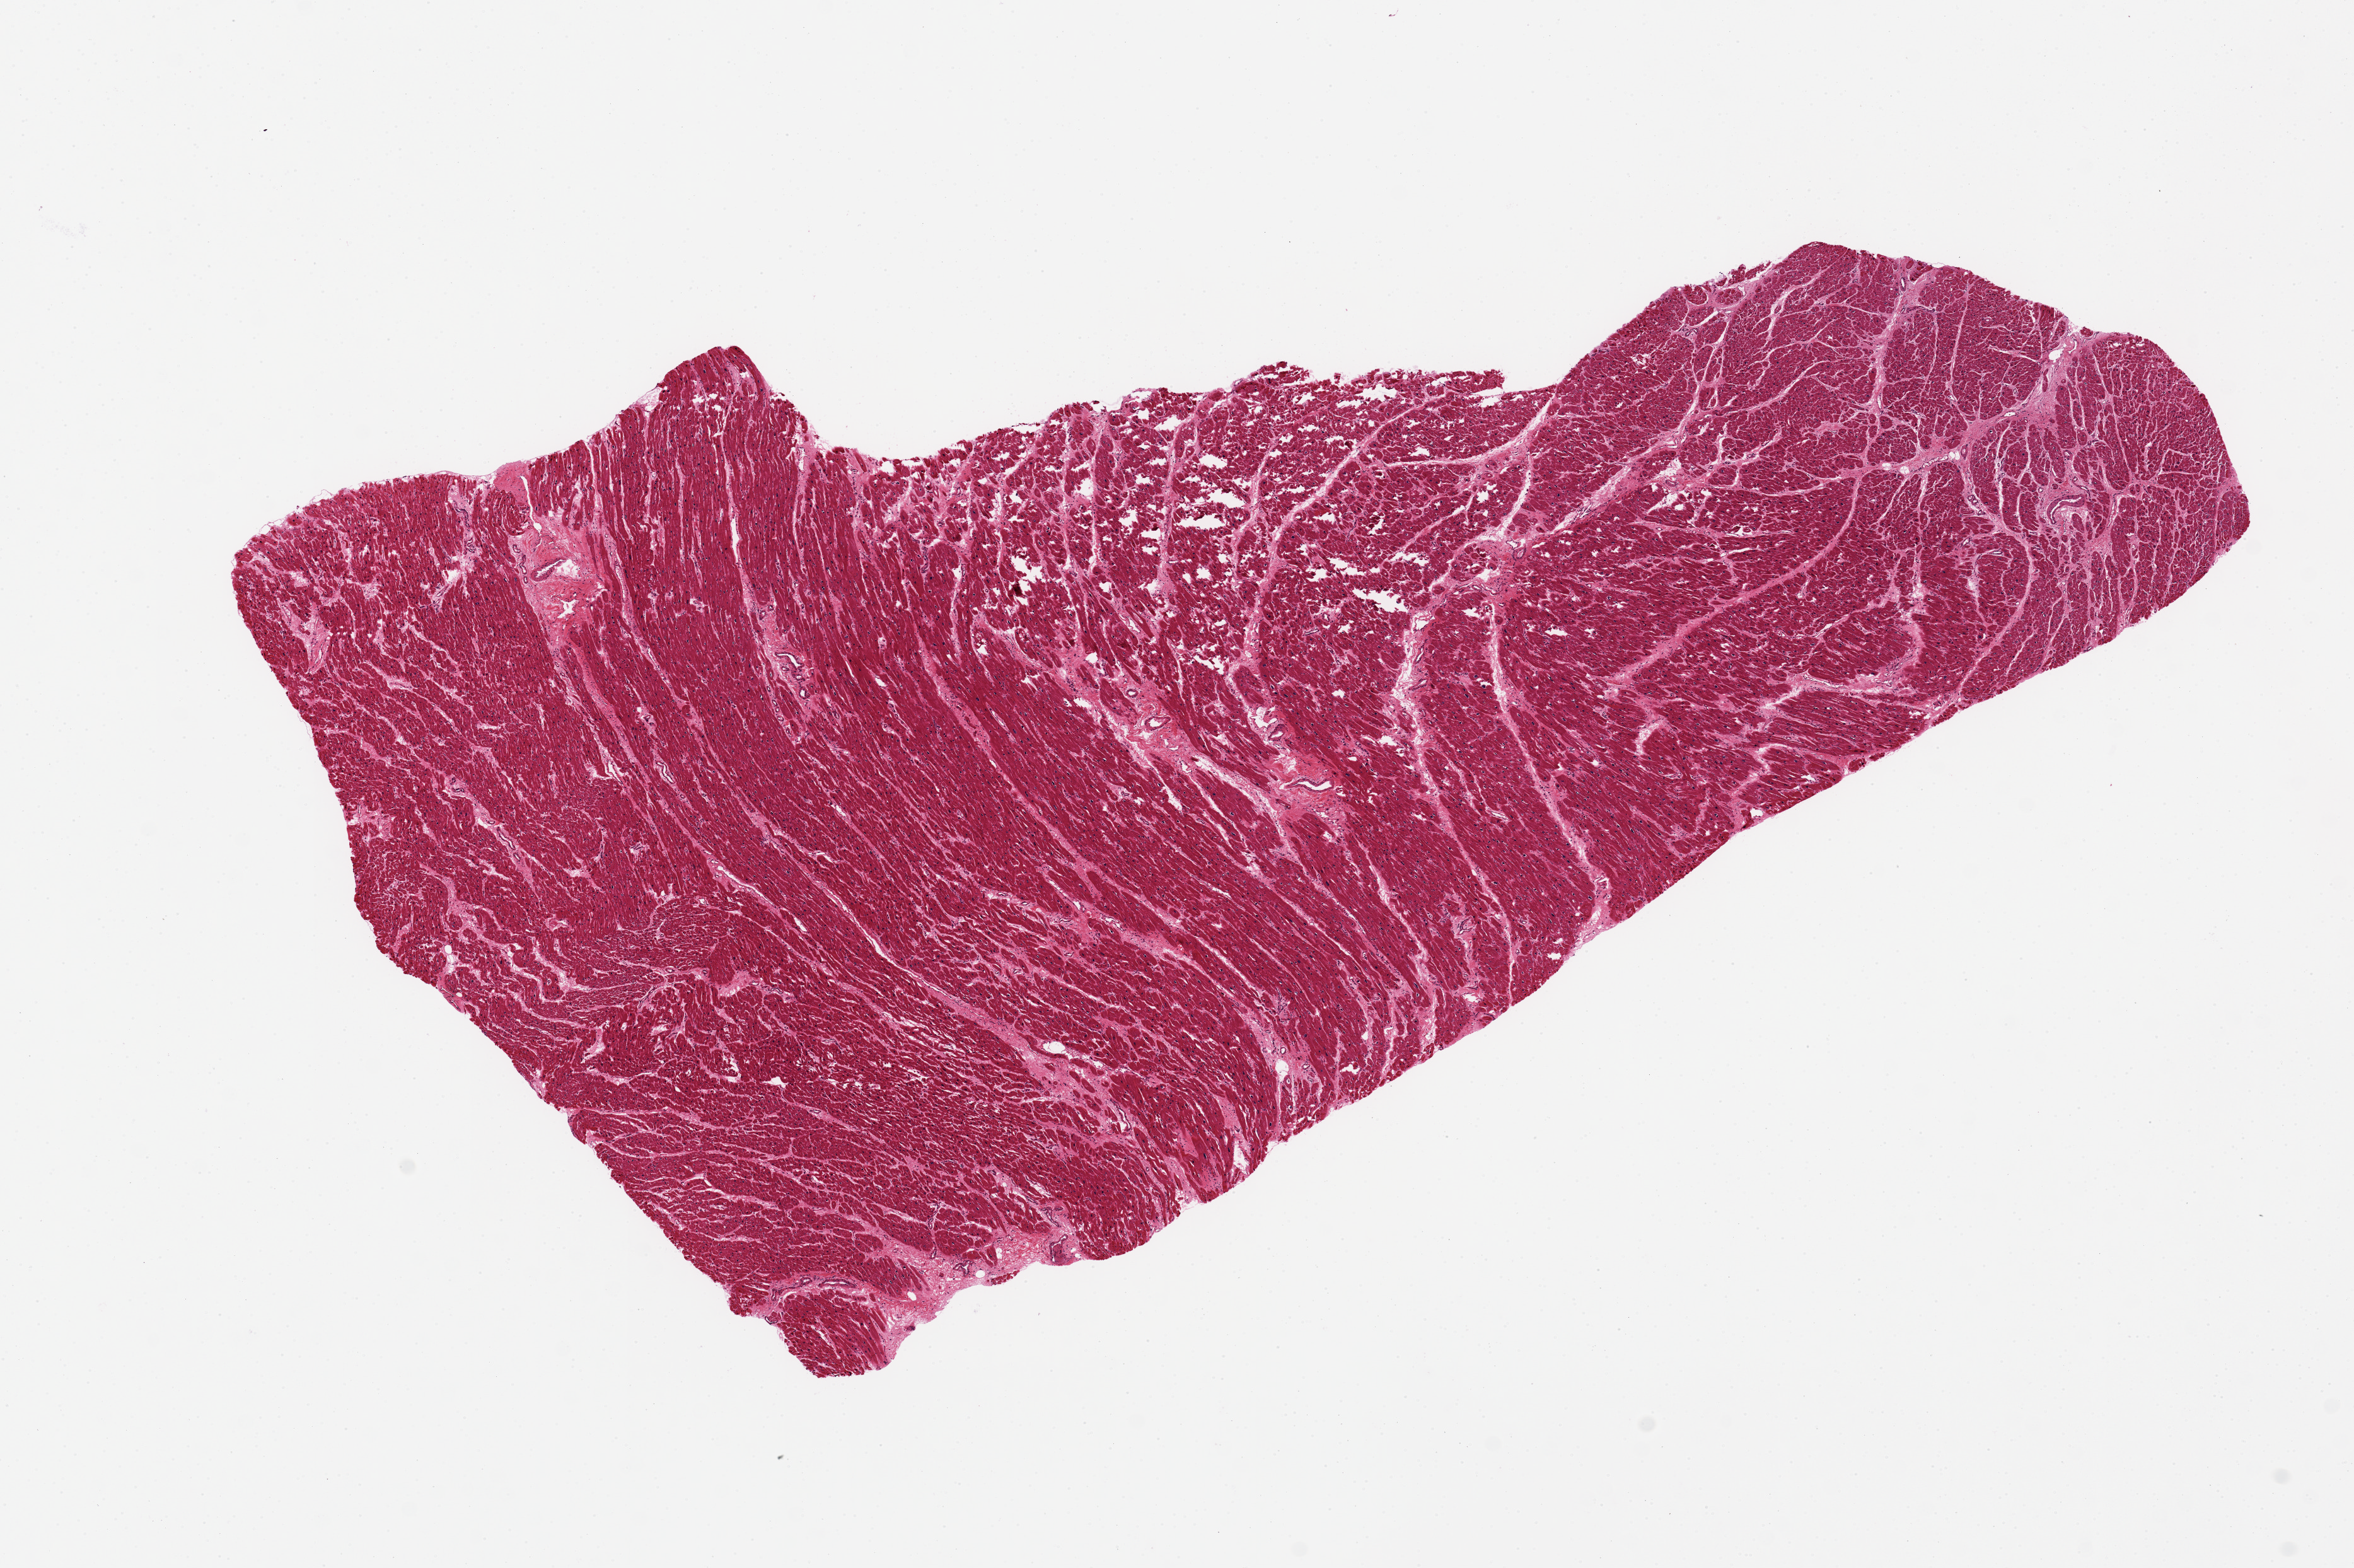
Digitized haematoxylin and eosin-stained section, shown as a low-resolution overview of the whole scanned area (about 14.8 x 9.8 mm, slide scanned at 20x). PAXgene-fixed, paraffin-embedded tissue. Sampled site (target tissue): heart. Donor tissue sample.
Review note (as recorded): Patchy ischemic changes. A number of central tears in specimen. 11x 6mm.